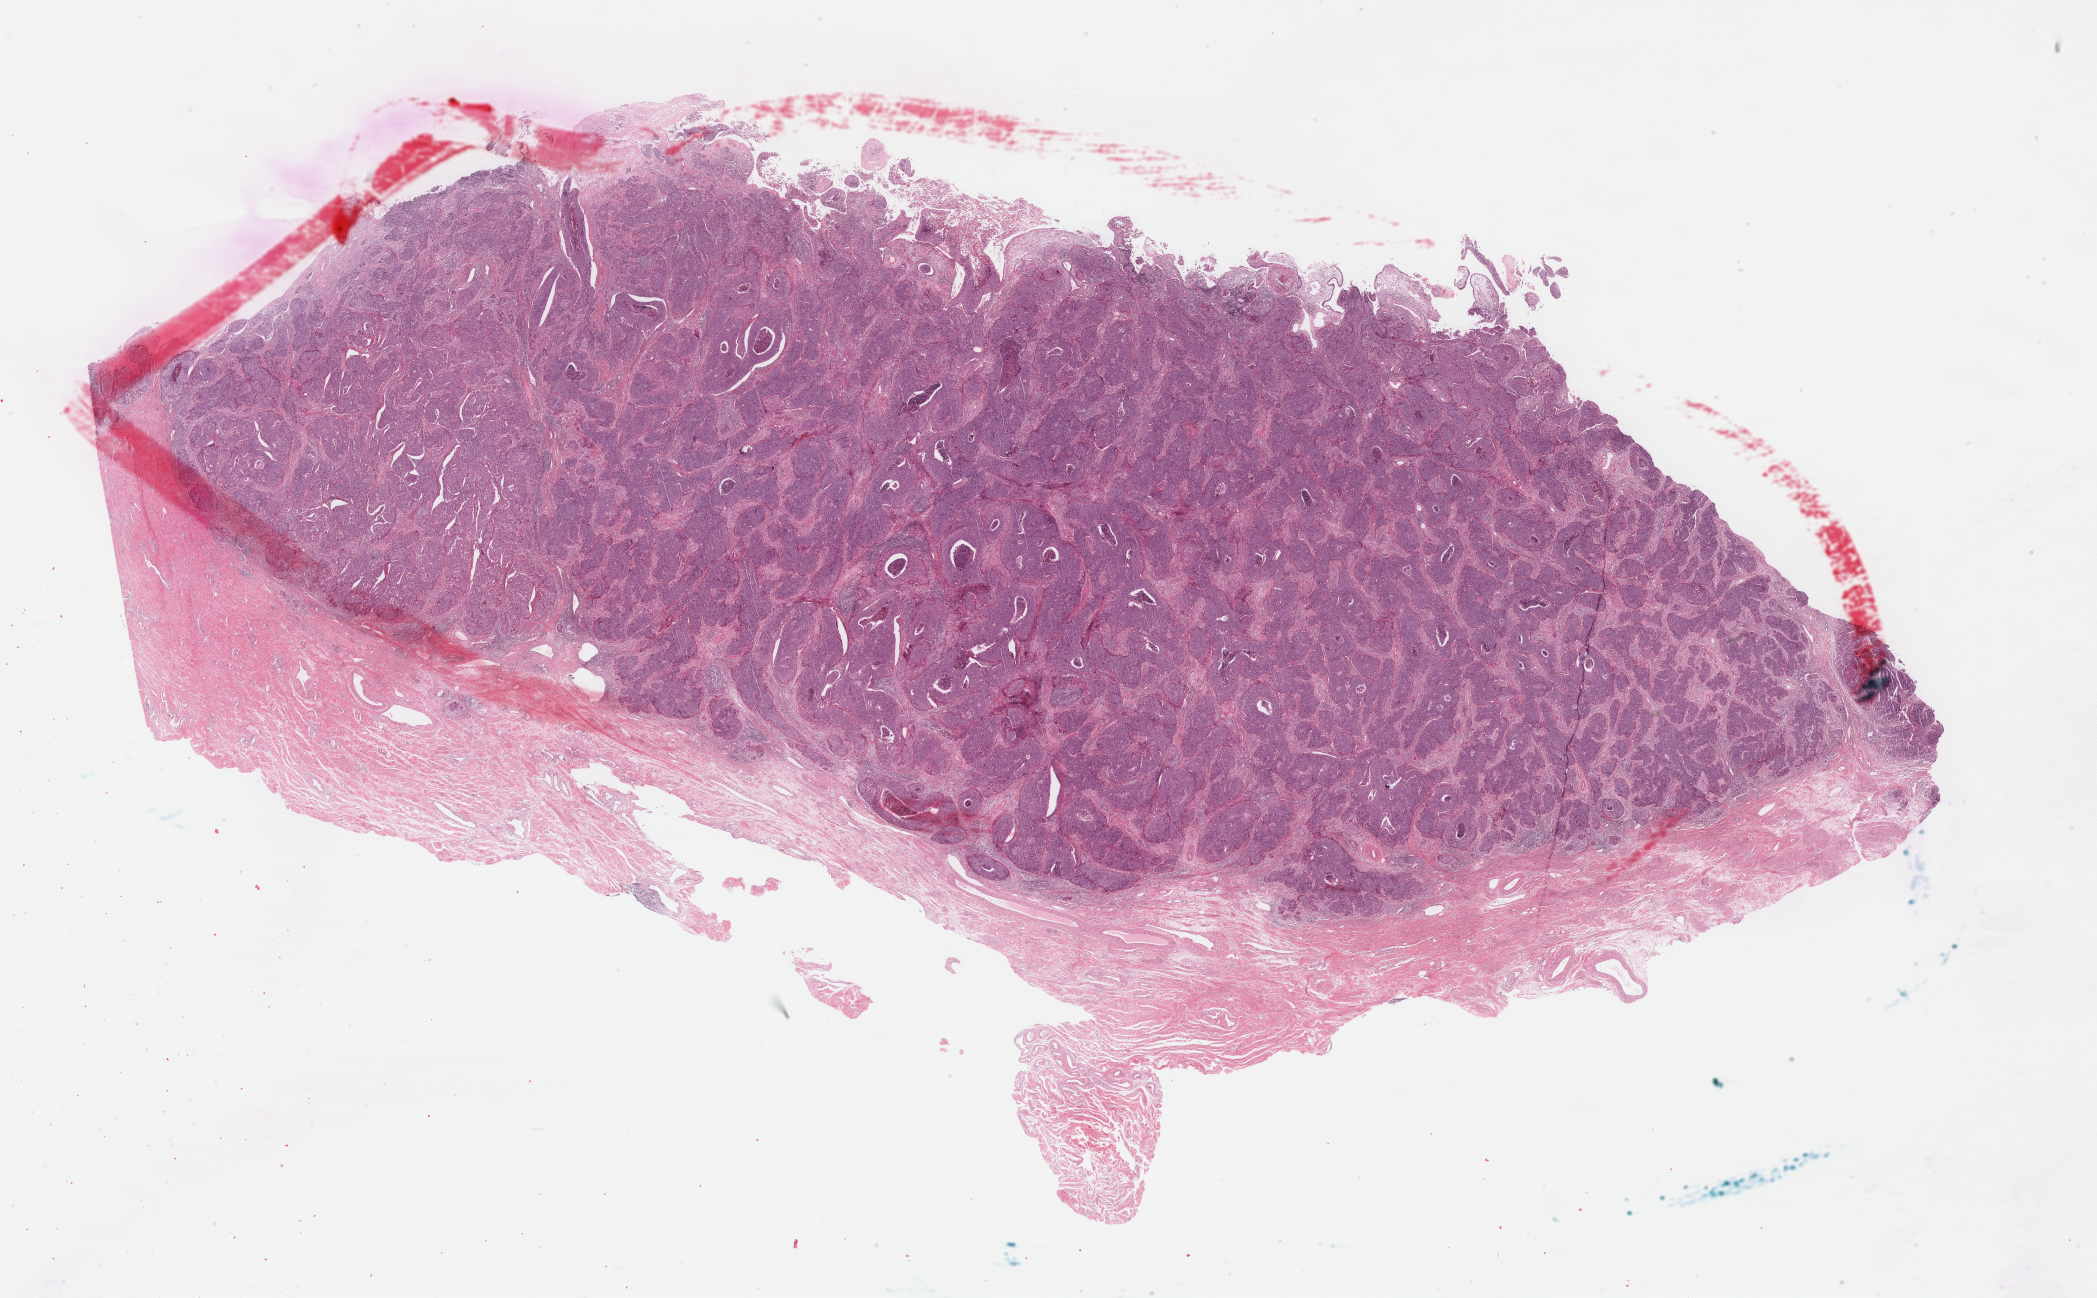
Digitized Hematoxylin and eosin (H&E) stained tissue section (whole slide), low-resolution overview of the scanned area, about 33.3 x 20.6 mm (acquisition: 40x scan), formalin-fixed paraffin-embedded (FFPE) diagnostic section, cervix, primary tumour sample. Female, age 60 years at initial diagnosis. Histologic grade: G2 (moderately differentiated).
FIGO stage: II. Pathologic diagnosis: Squamous cell carcinoma, NOS (cervix uteri). Lymph nodes positive (case pathology): 0 of 13 examined.